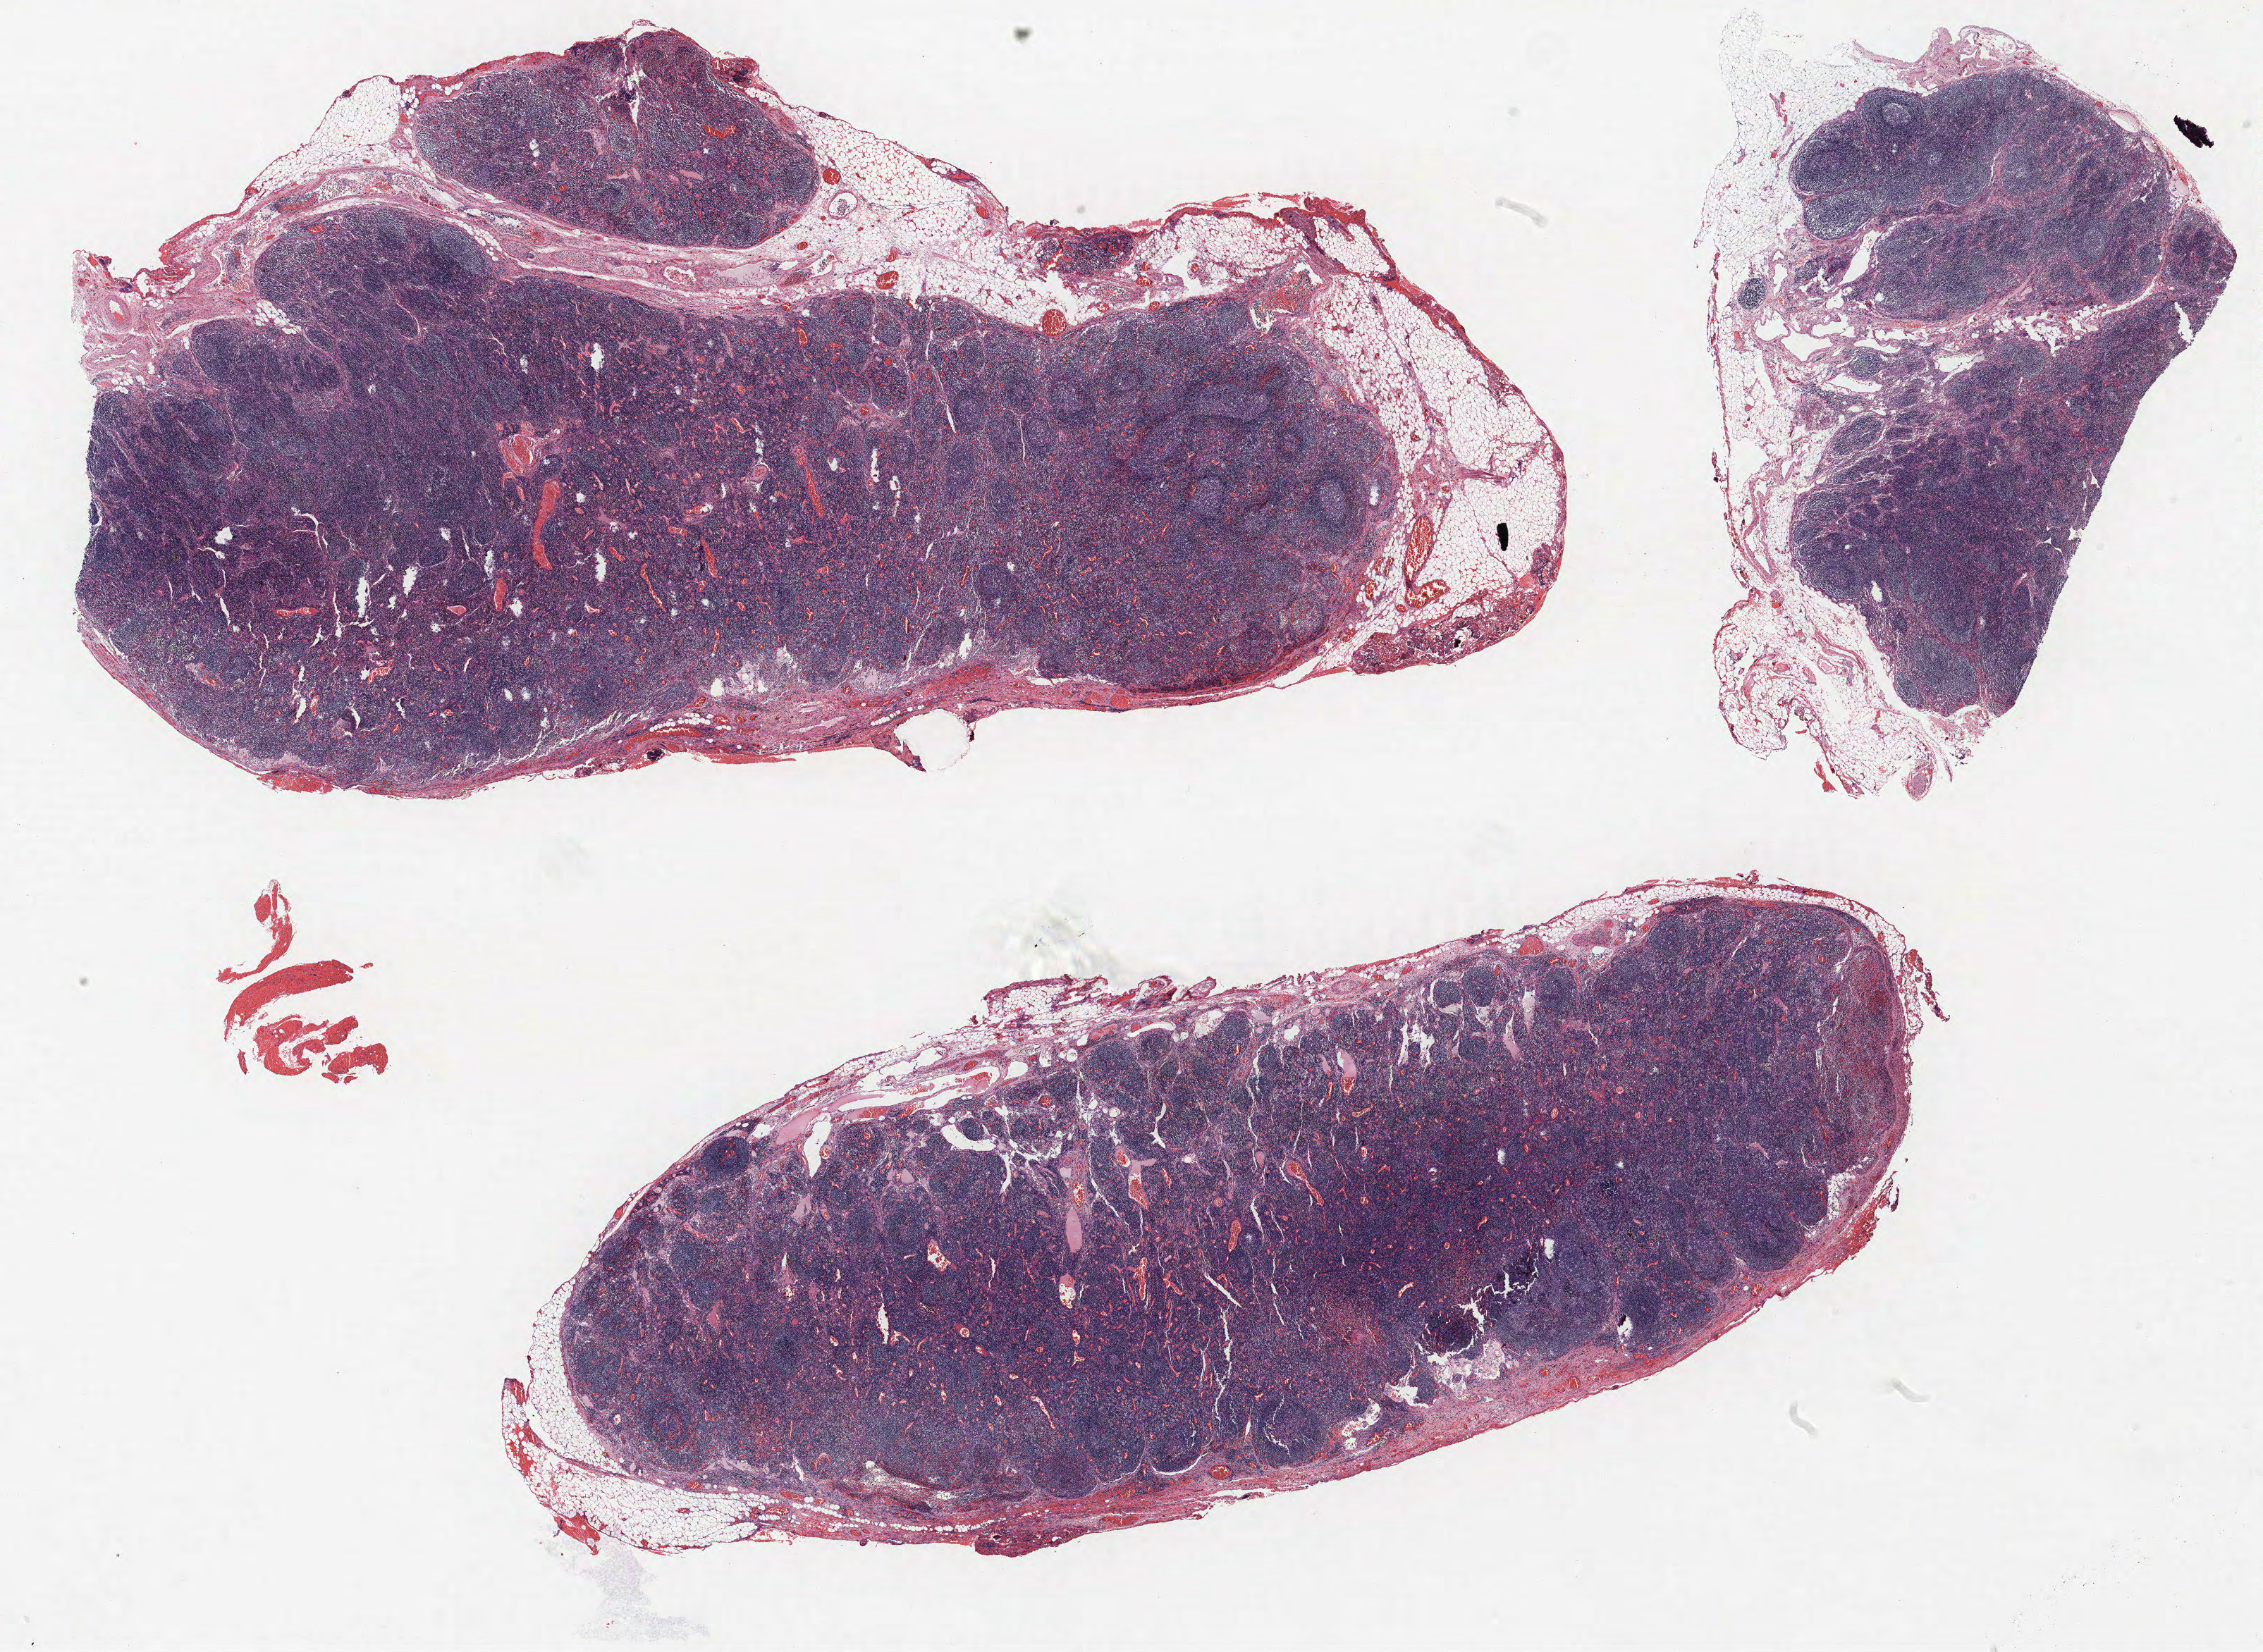
Whole-slide histology image, H&E-stained, a low-resolution overview of the entire scanned area, about 25.7 x 18.8 mm (from a 40x scan), FFPE section, lung. Female, age 56 at enrolment. Grade: poorly differentiated (G3).
* tumour size (pathology): 60 mm
* participant's lung-cancer diagnosis: Adenocarcinoma, NOS
* primary tumour location (clinical record): right lower lobe
* stage (AJCC 6th edition): IIB